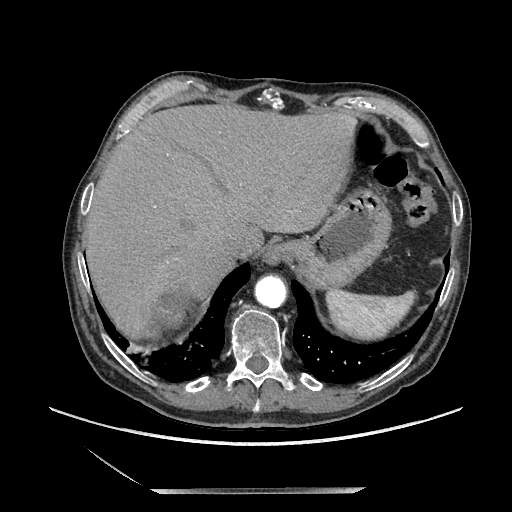
Contrast-enhanced abdominal CT, one axial slice; position 177 of 243 along the scan axis; soft-tissue window (W 400 / L 40 HU); 1.25 mm slice thickness; 512 × 512 image matrix, field of view 420 × 420 mm. Male patient. From the clinical record (not read from this slice): diagnosis: adrenocortical carcinoma; tumour side: right adrenal.
Outlined on this slice (semi-automatically segmented with operator editing):
- mass: bounding box <144,284,200,345> (left, top, right, bottom; pixels)